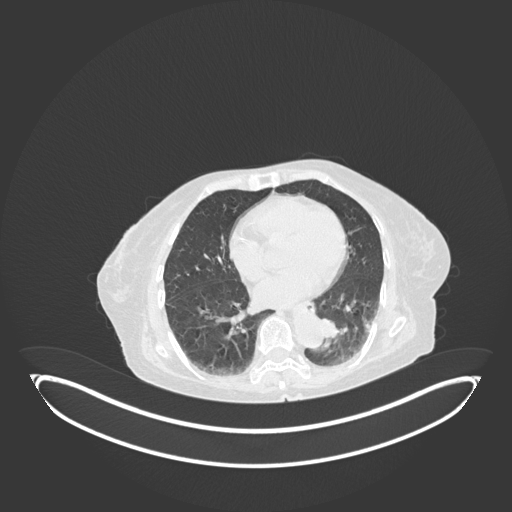
Chest CT, one axial slice; slice 38 of 189 in the series (ordered by position); reconstruction kernel B30f; 120 kVp; lung window (W 1500 / L -600 HU); 512 × 512 image matrix, field of view 500 × 500 mm. Female patient, age 82 years. From the clinical record (not read from this slice): clinical TNM (as recorded): T1b N0 M1.
Structures marked on this image (bounding box drawn by a radiologist):
- lung tumour (recorded histology: adenocarcinoma): bounding box [x1, y1, x2, y2] px = [321, 313, 348, 343]